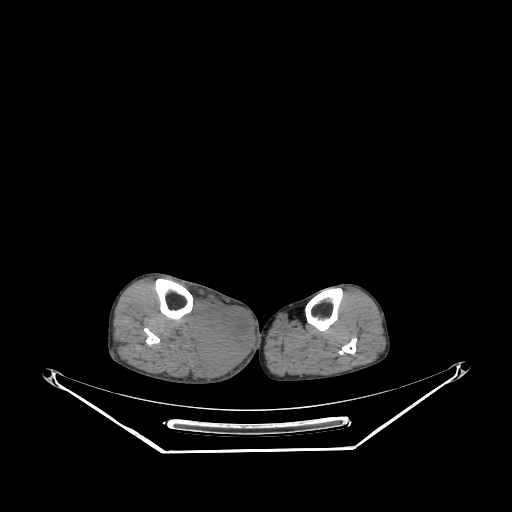
CT of an extremity soft-tissue mass (from a PET/CT study), one axial slice. Slice 136 of 267 in the series (ordered by position). Reconstruction kernel SOFT. Soft-tissue window (W 400 / L 40 HU). 3.75 mm slice thickness. 512 × 512 image matrix. Male patient. Case-level facts recorded for this patient, not image findings: histological type: pleiomorphic liposarcoma; grade: high; site of the primary tumour: right calf.
Structures marked on this image (expert contour drawn on MRI and transferred to this co-registered scan by the dataset authors):
- gross tumour volume including surrounding oedema: bounding box (x1, y1, x2, y2) in pixels: (194, 299, 254, 373)
- gross tumour volume (mass): (194, 304, 254, 366)